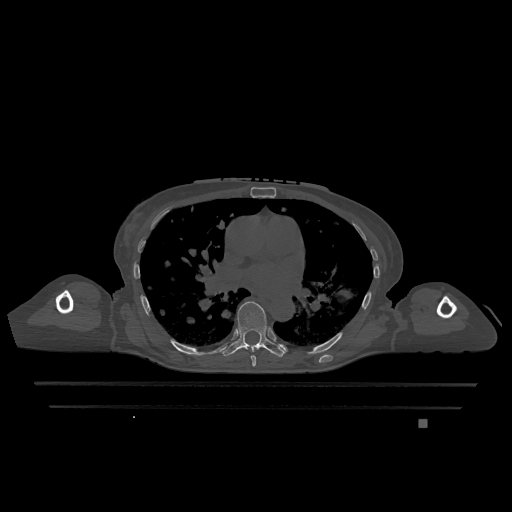
CT including the spine, one axial slice. Position 752 of 1317 along the scan axis. Bone window (W 1800 / L 400 HU). 512 × 512 image matrix, field of view 500 × 500 mm. Patient: female, 74 years. From the clinical record (not read from this slice): primary cancer: lung.
Annotated regions visible in this slice (semi-automatically segmented with operator editing):
- T6 vertebra: bounding box <251,355,256,367> (left, top, right, bottom; pixels)
- T7 vertebra: <221,301,286,358>